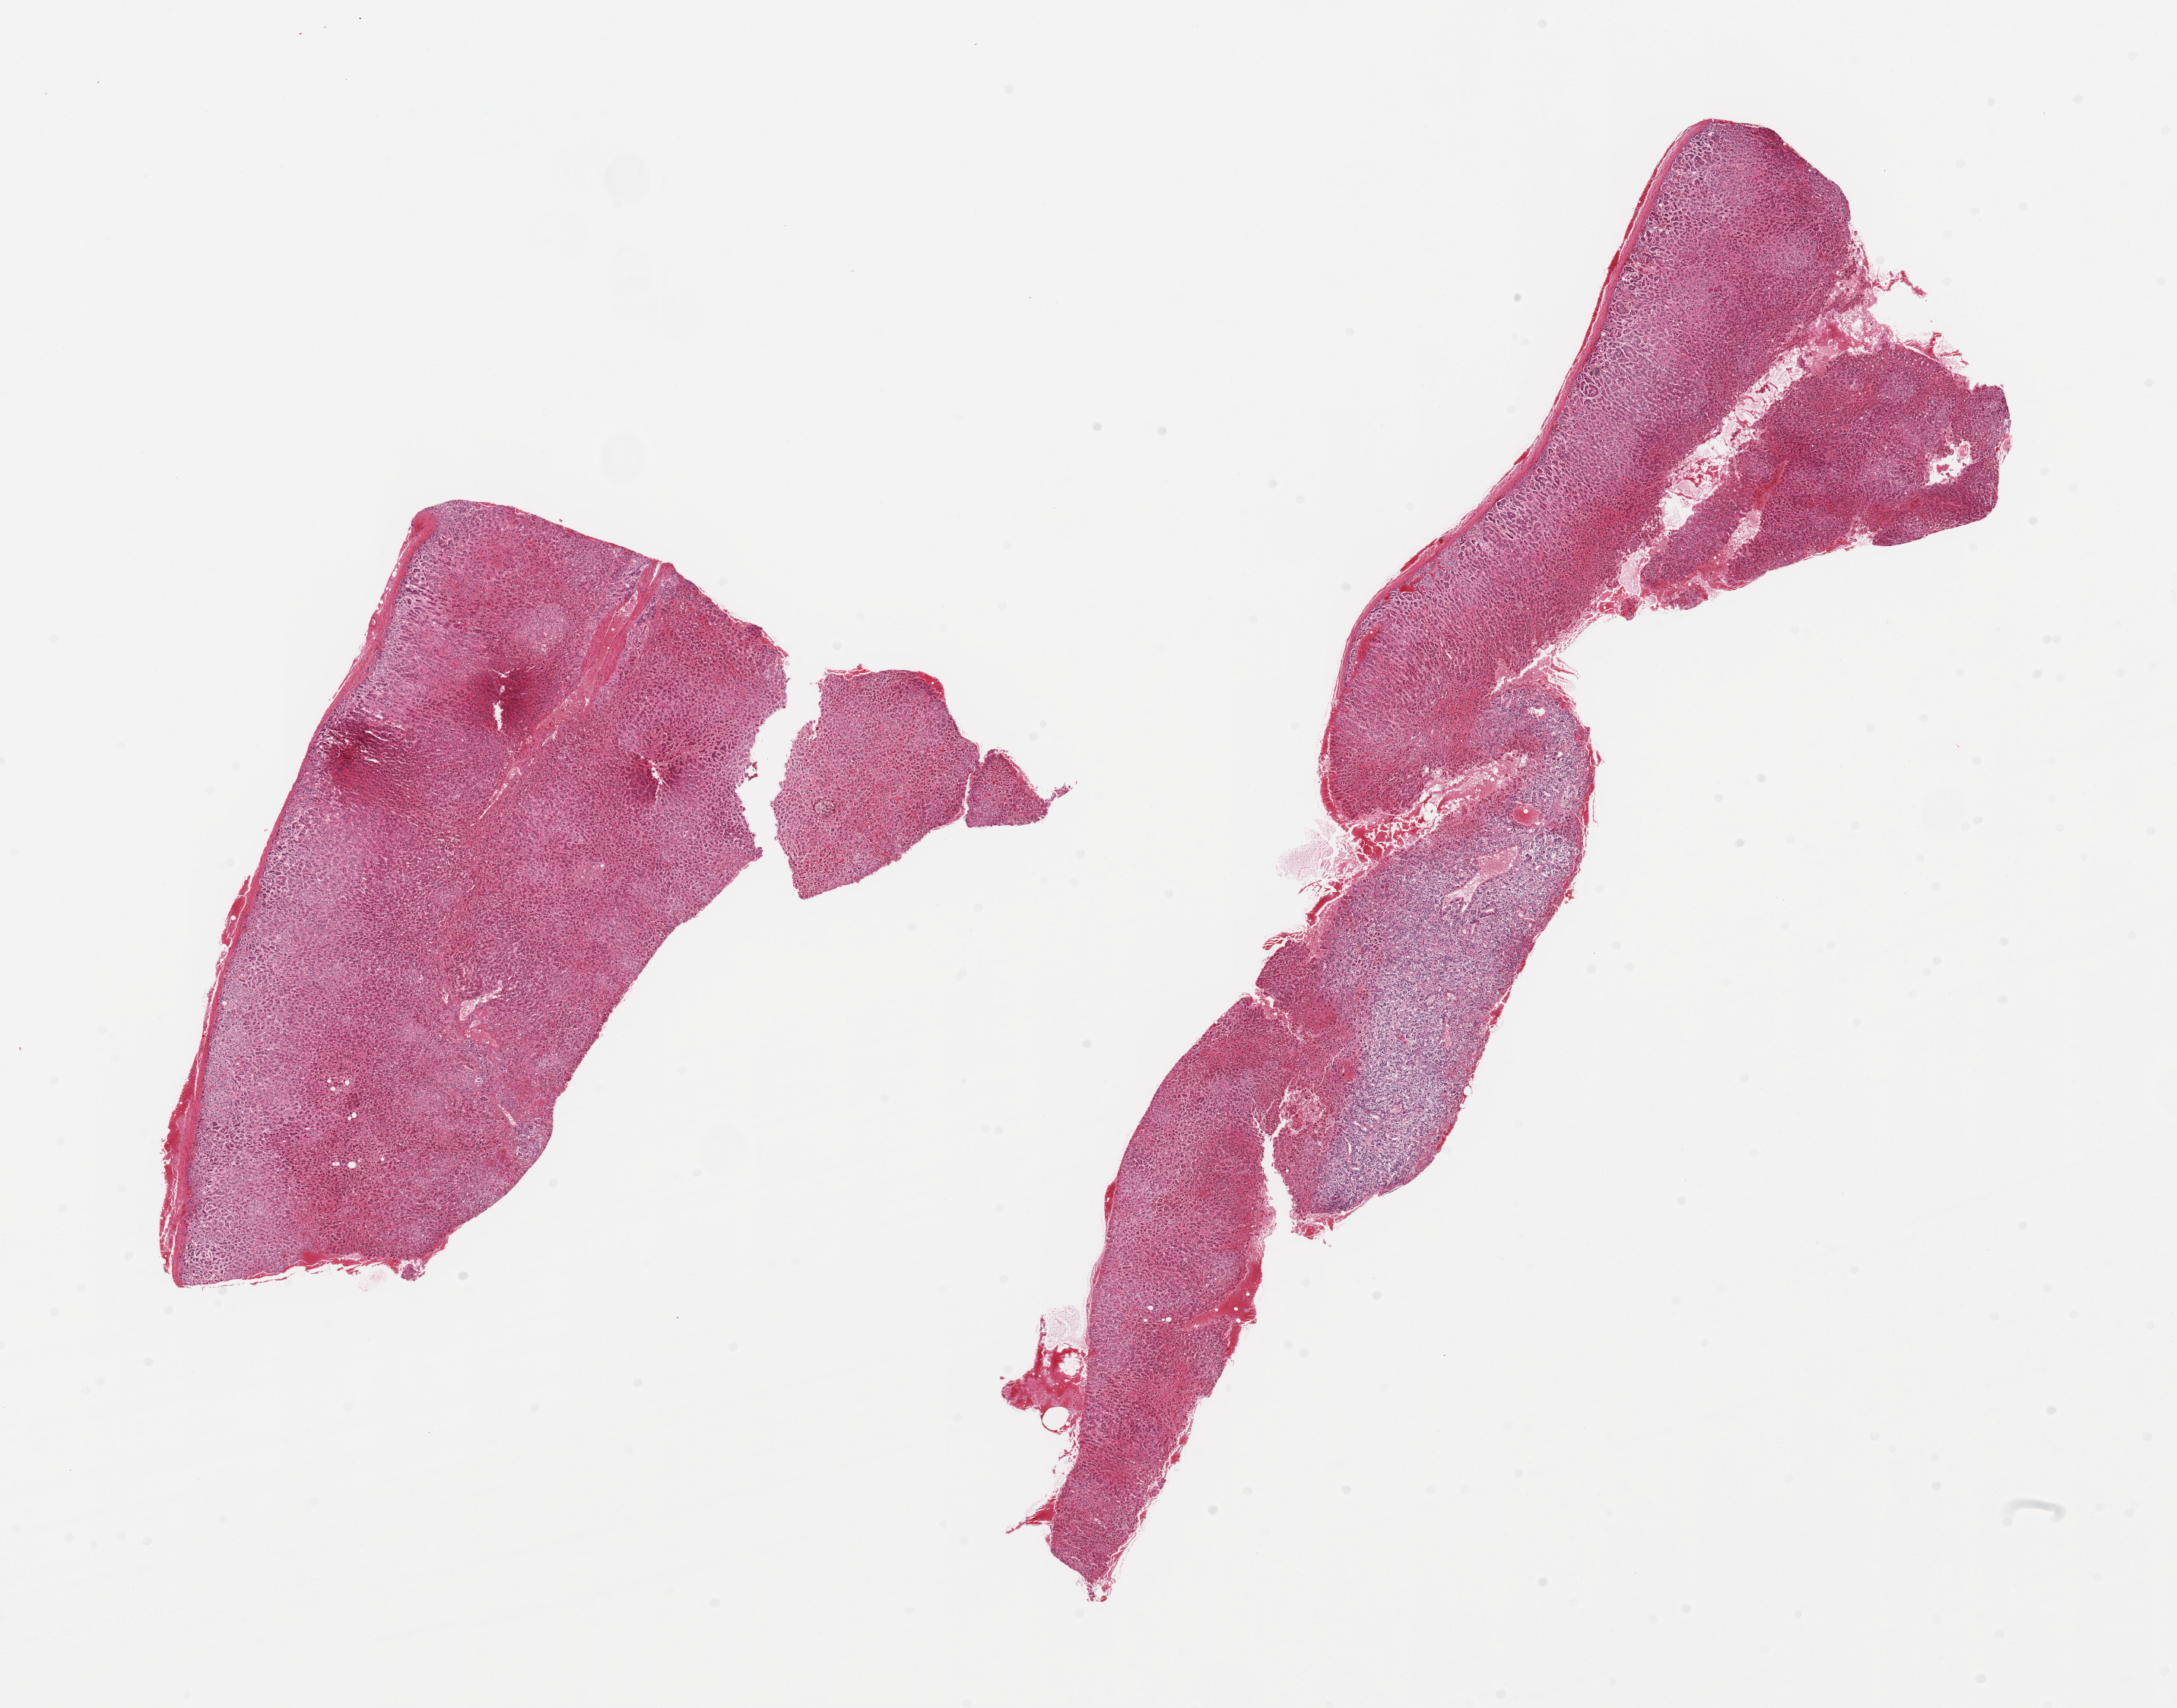
Digitized haematoxylin and eosin-stained section — low-resolution overview of the scanned area, about 22.6 x 17.8 mm (slide scanned at 20x); PAXgene-fixed paraffin-embedded (PFPE) section; sampled site (target tissue): adrenal gland; tissue donor sample.
Review note (as recorded): 2 pieces; cortex and medulla.